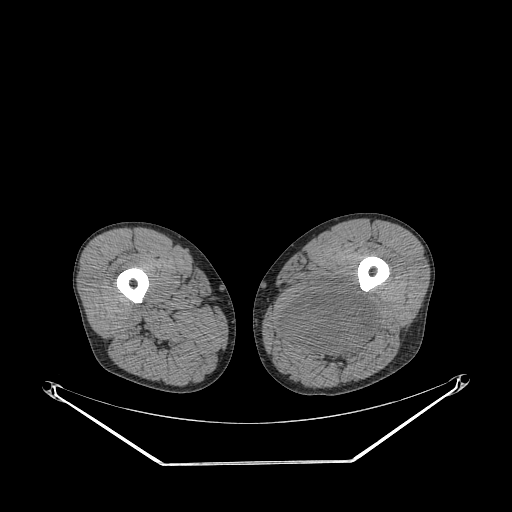
CT of an extremity soft-tissue mass (from a PET/CT study), one axial slice; slice 244 of 267 in the series (ordered by position); reconstruction kernel STANDARD; soft-tissue window (W 400 / L 40 HU); 512 × 512 image matrix, field of view 500 × 500 mm. Male patient. Case-level facts recorded for this patient, not image findings: histological type: undifferentiated pleomorphic liposarcoma; grade: high; site of the primary tumour: left thigh.
Outlined on this slice (expert contour drawn on MRI and transferred to this co-registered scan by the dataset authors):
- gross tumour volume including surrounding oedema: box from (x=276, y=285) to (x=375, y=362) px
- gross tumour volume (mass): (x=283, y=285)–(x=375, y=352)